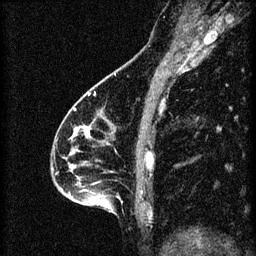
Breast MRI (dynamic contrast-enhanced), one sagittal slice; position 28 of 60 along the scan axis; 3 images stored at this slice position (order not interpretable as contrast timing); 1.5 T; TE 4.2 ms, TR 8.2 ms; 256 × 256 image matrix, field of view 180 × 180 mm. Patient: female, 46 years.
Structures marked on this image (semi-automatically segmented with operator editing):
- analysis volume of interest (the breast-tissue region the enhancement analysis was run in; not a lesion): bounding box <55,114,148,209> (left, top, right, bottom; pixels)
- tumour enhancement mask (voxels above the 70 % enhancement threshold inside the analysis volume of interest): <74,126,90,137>